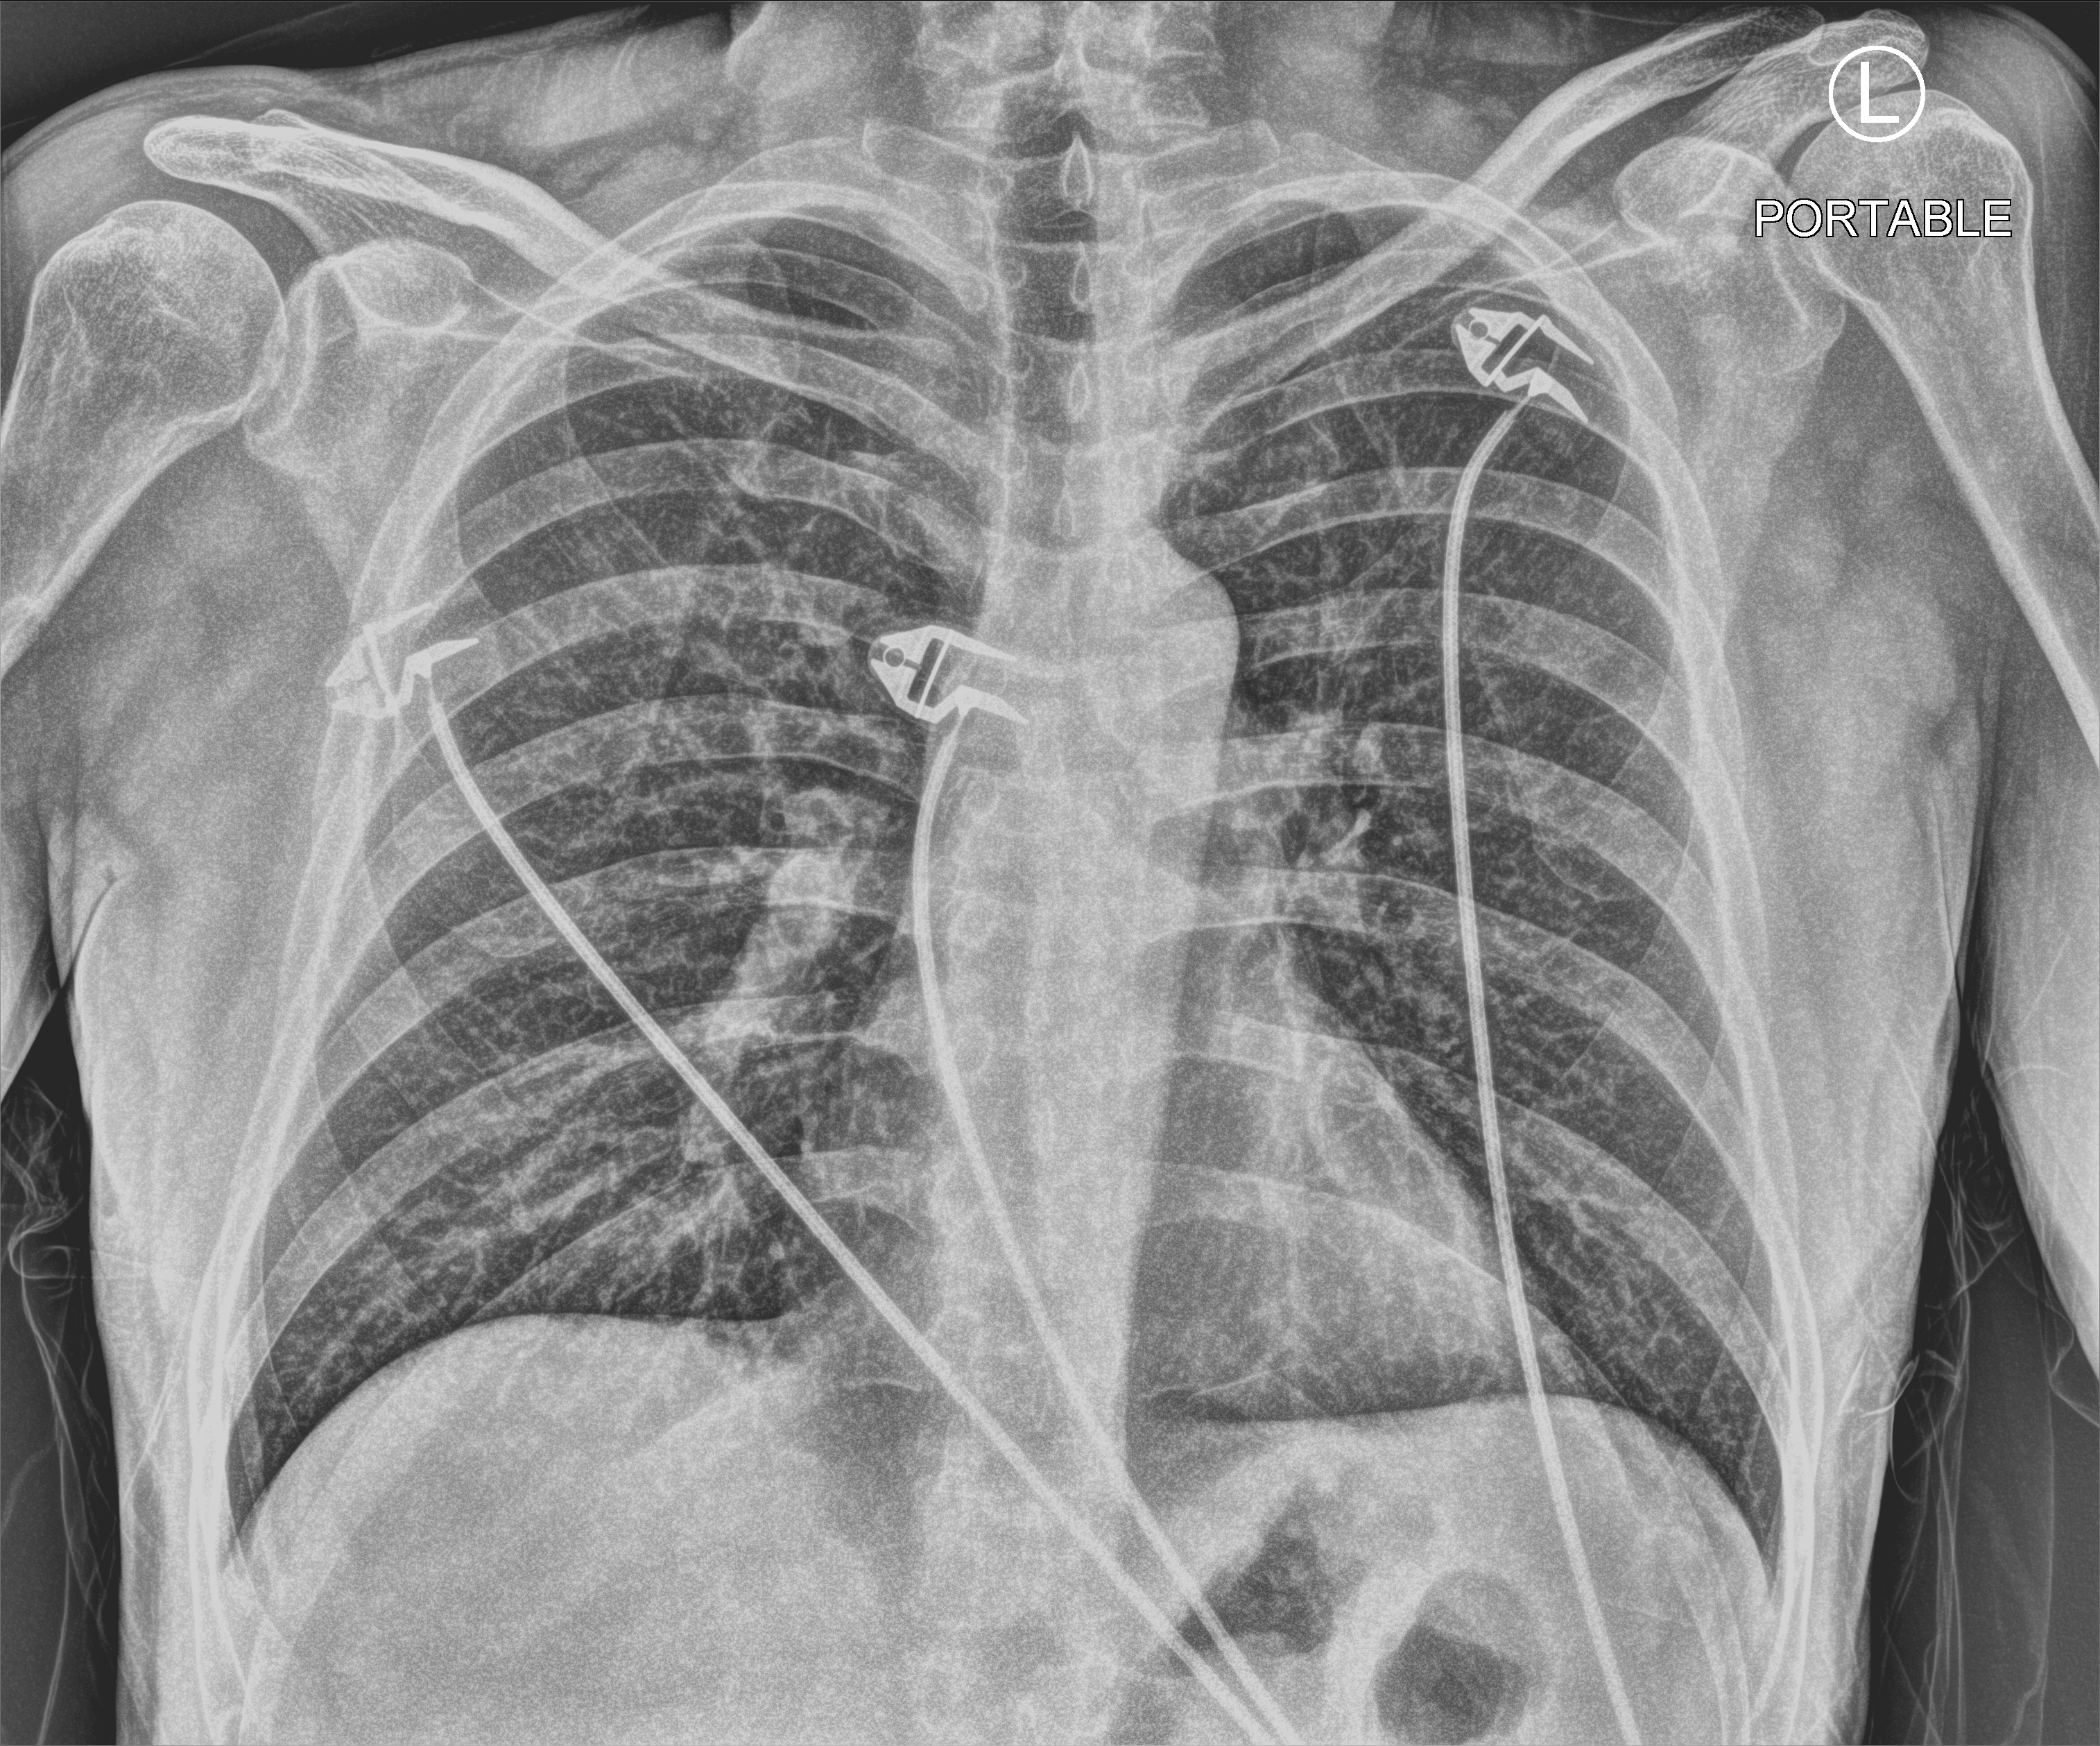
Portable chest radiograph, anteroposterior (AP) projection. Patient hospitalised with COVID-19; male, aged 18–59 years.
Hospital-stay facts (about this admission, not read from this image; timing relative to this image not recorded): admitted to intensive care during this hospital stay: no; length of hospital stay: 4 days; mechanically ventilated during this hospital stay: no.